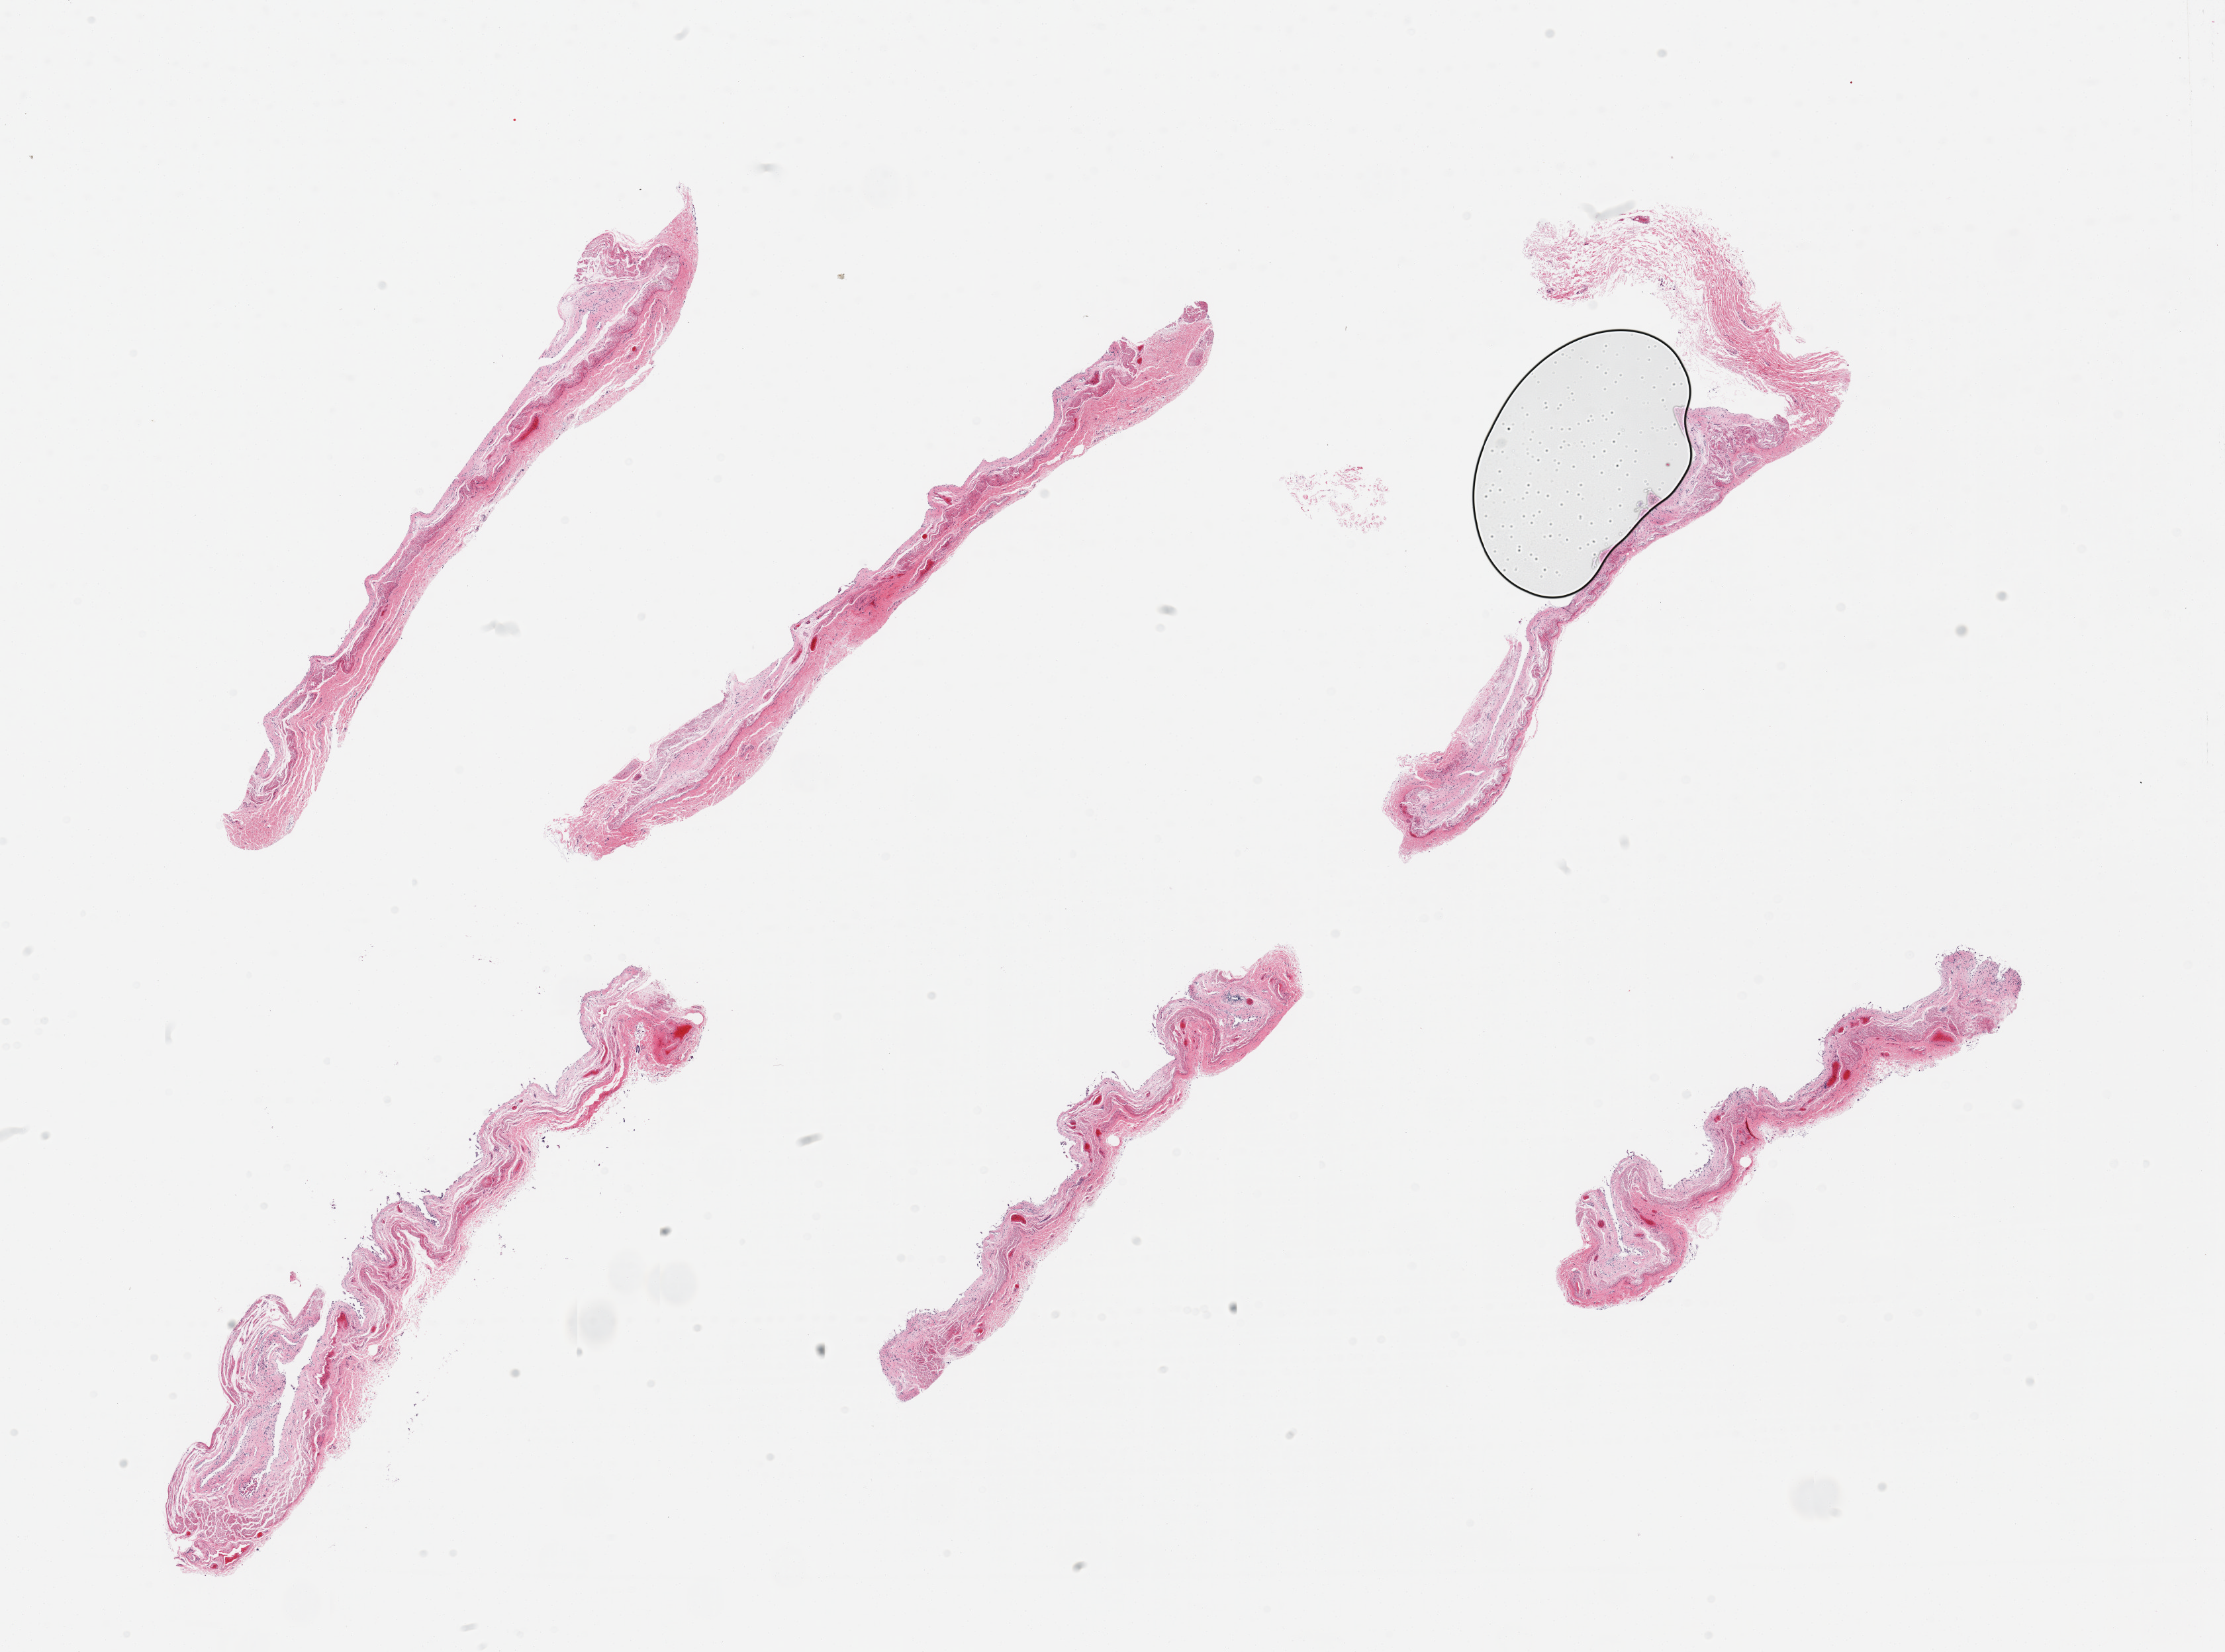
Whole-slide image, hematoxylin and eosin (H&E) stain, low-resolution overview of the scanned area, about 26.6 x 19.7 mm (from a 20x scan). PAXgene-fixed, paraffin-embedded tissue. Sampled site (target tissue): esophageal mucous membrane. Tissue donor sample. Donor: male.
Review note (as recorded): 6 pieces, mucosa completely sloughed/autolyzed.